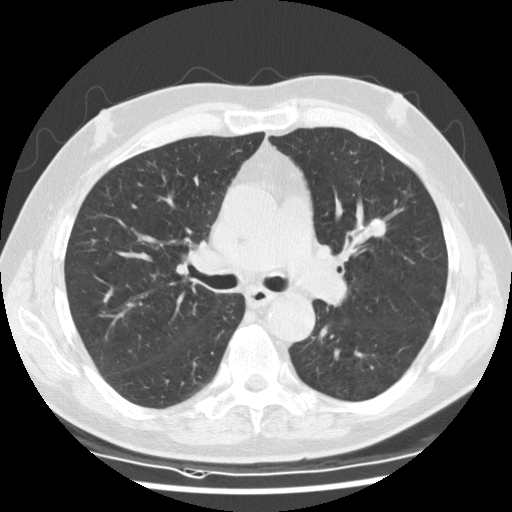
Low-dose screening chest CT, one axial slice. Position 77 of 135 along the scan axis. Lung window (W 1500 / L -600 HU). 2.5 mm slice thickness. 512 × 512 image matrix.
Annotated regions visible in this slice (expert manual segmentation):
- lesion 1 (tumor, upper lobe of left lung): bounding box [x1, y1, x2, y2] px = [368, 218, 386, 237]